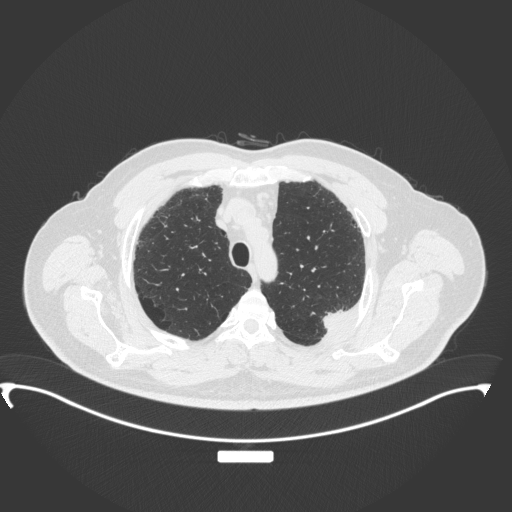
Chest CT, one axial slice; position 288 of 350 along the scan axis; reconstruction kernel B31f; lung window (W 1500 / L -600 HU); 1 mm slice thickness; 512 × 512 image matrix, field of view 459 × 459 mm. Male patient, age 64 years. Case-level facts recorded for this patient, not image findings: clinical TNM (as recorded): T1c N1 M1.
Annotated regions visible in this slice (bounding box drawn by a radiologist):
- lung tumour (recorded histology: adenocarcinoma): bounding box [x1, y1, x2, y2] px = [314, 304, 350, 331]